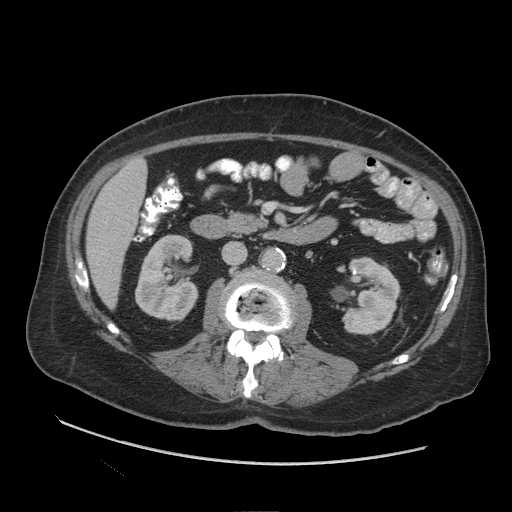
Contrast-enhanced abdominal CT (liver protocol), one axial slice. Slice 32 of 109 in the series (ordered by position). Reconstruction kernel STANDARD. 140 kVp. Soft-tissue window (W 400 / L 40 HU). 2.5 mm slice thickness. 512 × 512 image matrix, field of view 420 × 420 mm. From the clinical record (not read from this slice): diagnosis: hepatocellular carcinoma (patient treated with transarterial chemoembolisation; whether this scan precedes or follows treatment is not stated here); TNM stage (as recorded): Stage-I; Child-Pugh class: A.
Structures marked on this image (semi-automatic segmentation, software-assisted and operator-edited):
- liver parenchyma outside the tumour (the mass and vessels are separate outlines, so this box may not span the whole liver): bounding box [x1, y1, x2, y2] px = [86, 158, 146, 308]